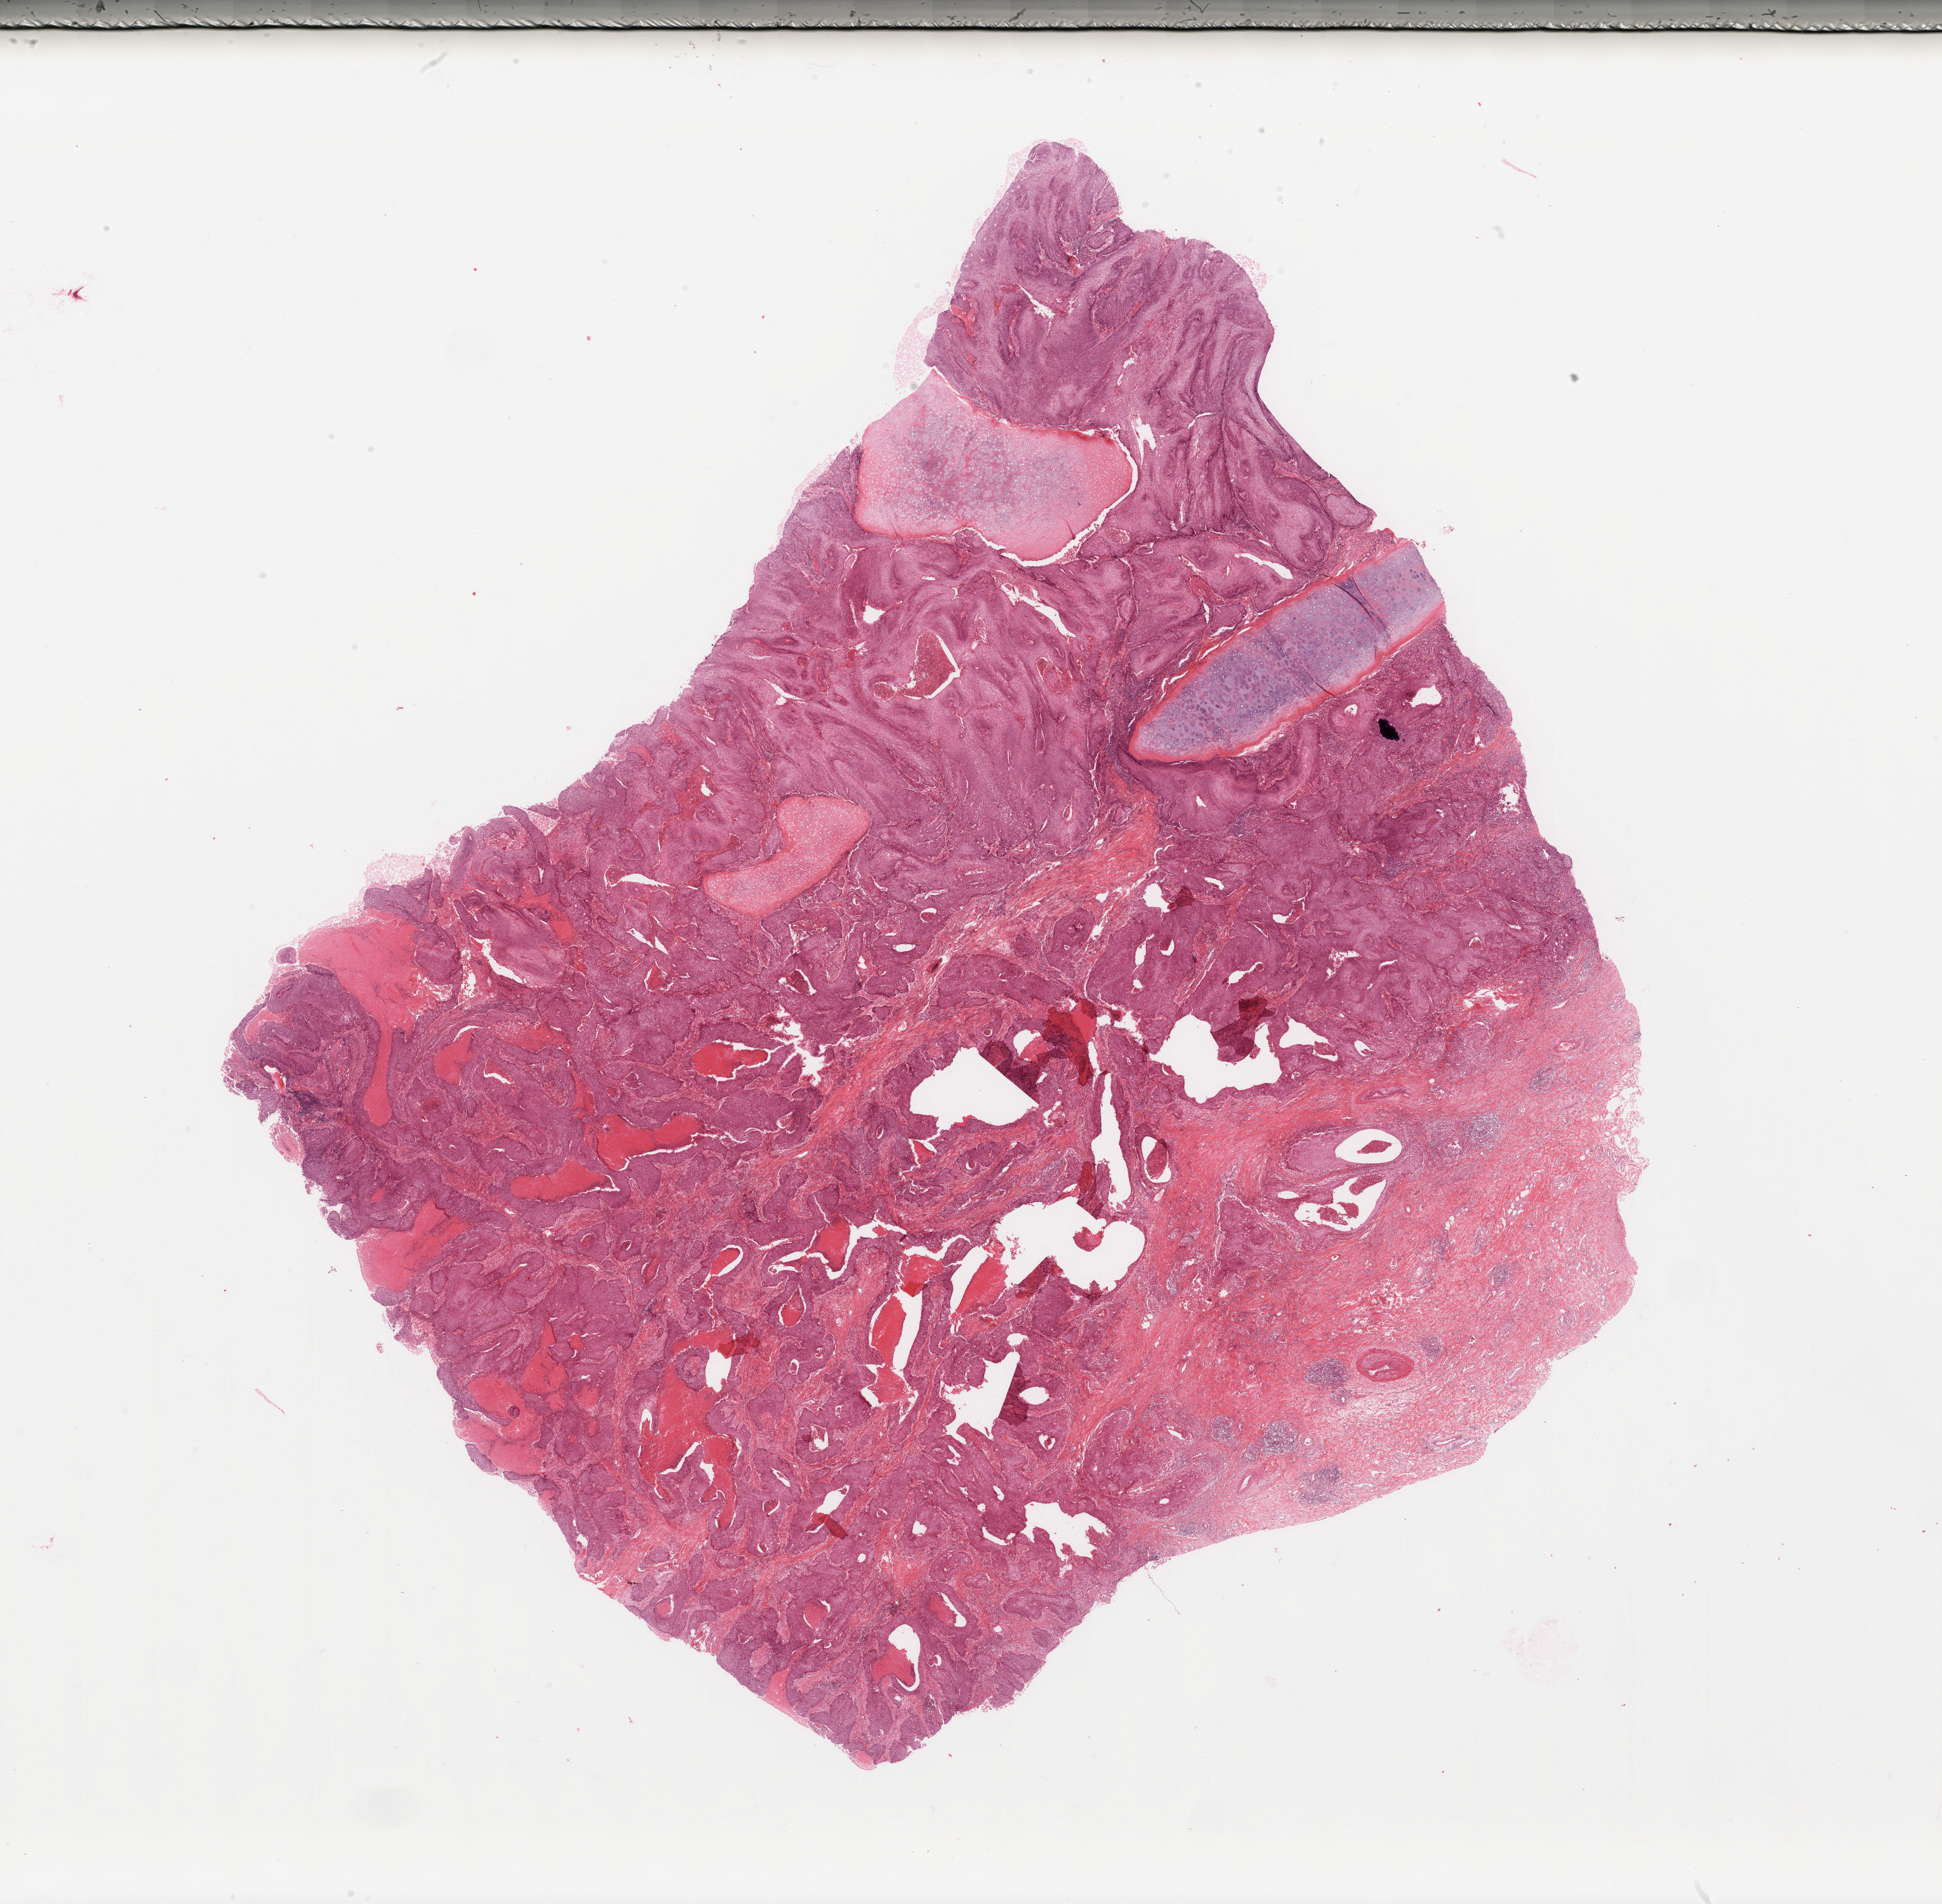
Digitized H&E-stained tissue section (whole slide), whole scanned area (about 24.6 x 24.1 mm, slide scanned at 20x) shown as a low-resolution overview, tumour tissue sample, lung. Patient: male, age 64 years. Histologic grade: G3 (poorly differentiated).
Diagnosis: Squamous cell carcinoma, NOS. AJCC pathologic stage: IB.